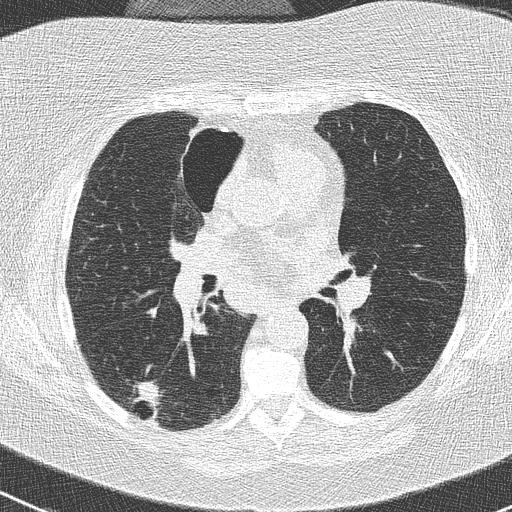
Low-dose screening chest CT, axial slice; first (baseline) screen; lung window (W 1500 / L -600 HU). Female participant, aged 74 years at enrolment. Former smoker at enrolment.
Lesion marked by an expert reader, bounding box (x1, y1, x2, y2) in pixels: (120, 374, 174, 429). The screening reader recorded 3 non-calcified nodules or masses ≥4 mm on this exam (right lower lobe, right upper lobe, left lower lobe); which of them this box marks is not recorded. Official screen result: positive, change unspecified: nodule(s) >= 4 mm or enlarging nodule(s), mass(es), or other non-specific abnormalities suspicious for lung cancer. Later outcome: lung cancer diagnosed 16 days after this screen — non-small cell carcinoma, right lower lobe, poorly differentiated (G3), stage IIIA (AJCC 6th edition), 28 mm at pathology.